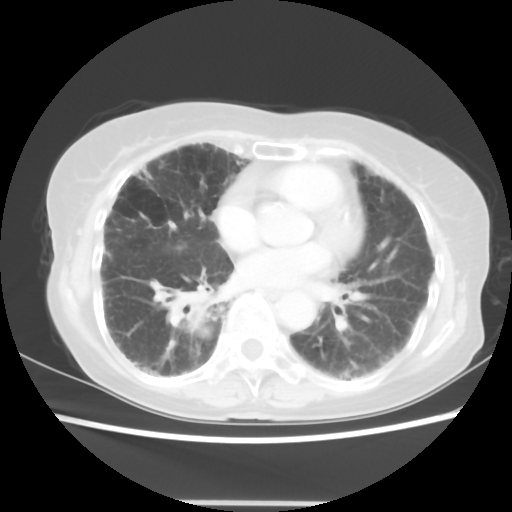
Chest CT, one axial slice; position 24 of 52 along the scan axis; reconstruction kernel STANDARD; 120 kVp; lung window (W 1500 / L -600 HU); 5 mm slice thickness; 512 × 512 image matrix, field of view 325 × 325 mm. Female patient, age 71 years. Case-level facts recorded for this patient, not image findings: clinical TNM (as recorded): T3 N0 M0.
Outlined on this slice (bounding box drawn by a radiologist):
- lung tumour (recorded histology: squamous cell carcinoma): bounding box <169,291,221,338> (left, top, right, bottom; pixels)